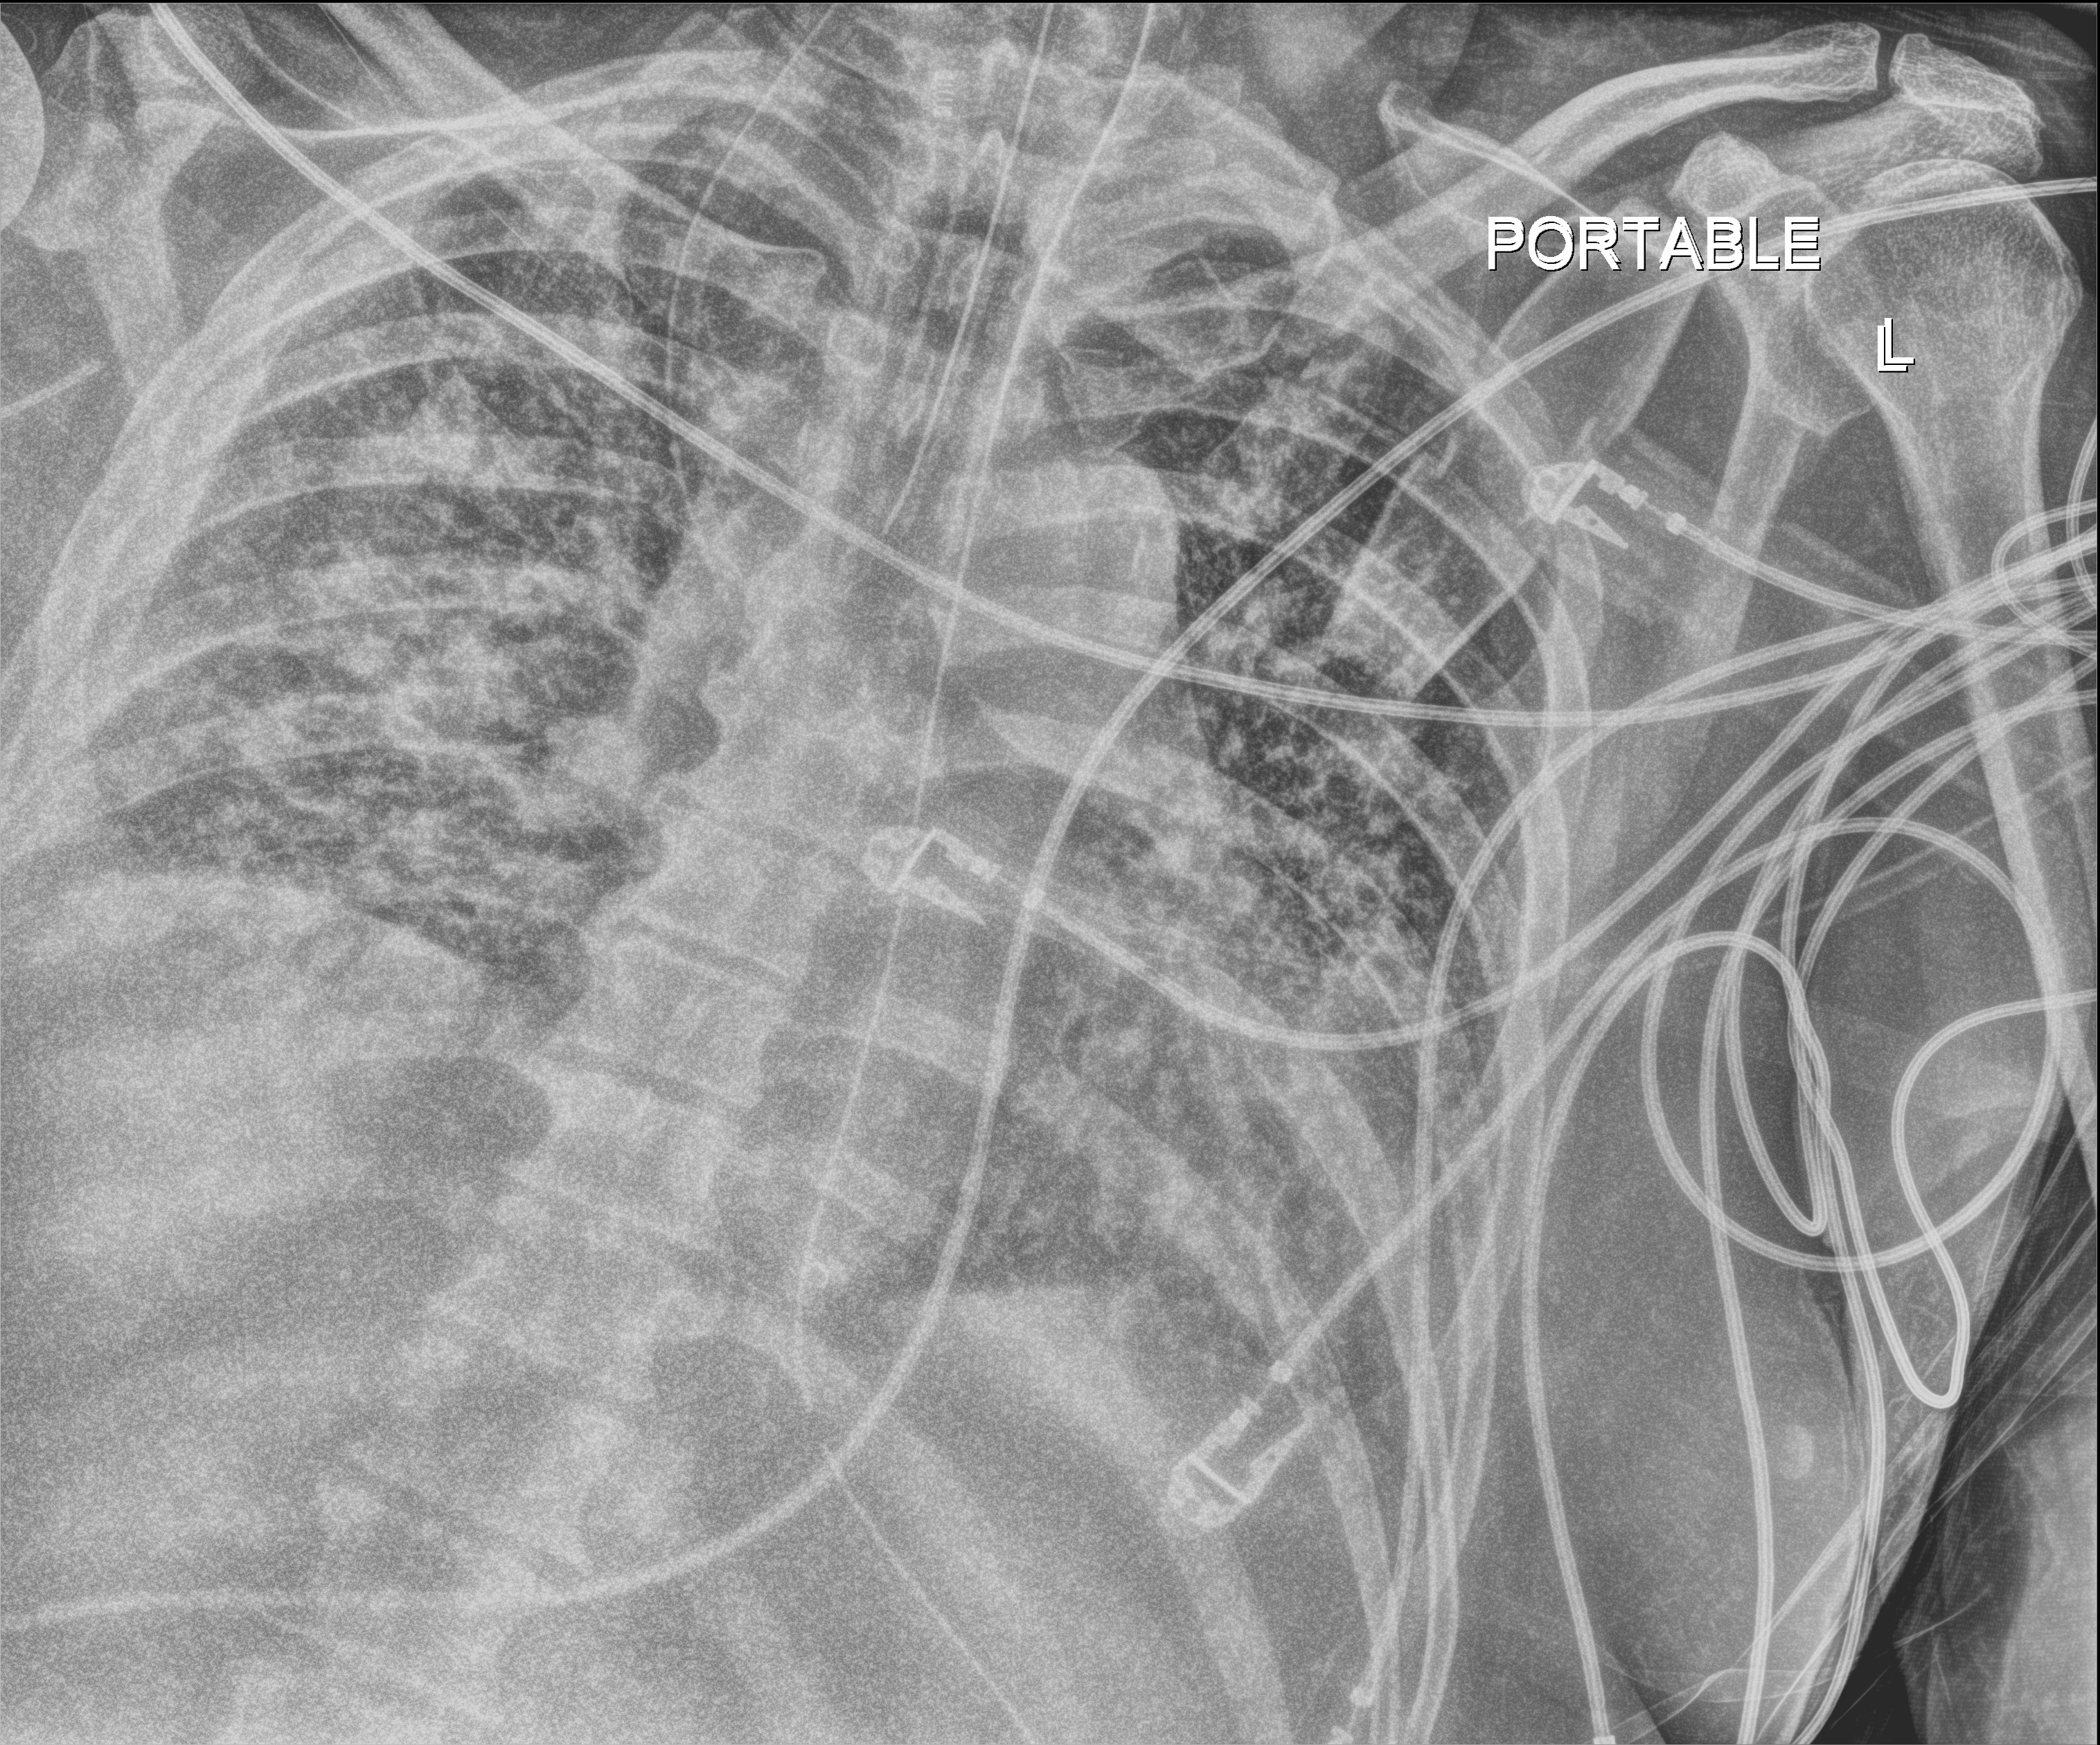
Bedside chest radiograph (digital radiography). Male patient hospitalised with COVID-19, age 60–74 years.
Hospital-stay facts (about this admission, not read from this image; timing relative to this image not recorded): admitted to intensive care during this hospital stay: yes; length of hospital stay: 40 days; mechanically ventilated during this hospital stay: yes.